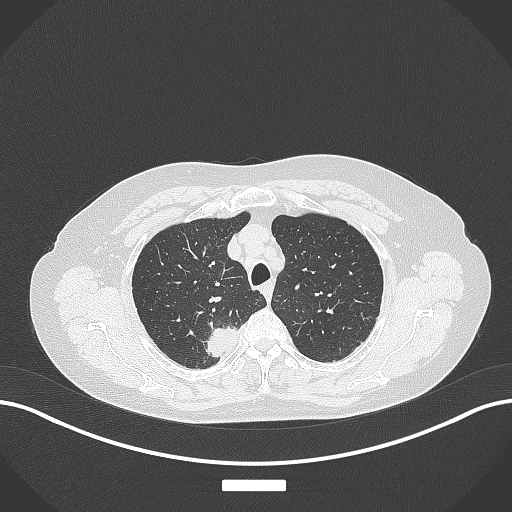
Chest CT, one axial slice. Position 314 of 357 along the scan axis. Reconstruction kernel B70f. 120 kVp. Lung window (W 1500 / L -600 HU). 1 mm slice thickness. 512 × 512 image matrix, field of view 400 × 400 mm. Patient: female, 62 years. From the clinical record (not read from this slice): clinical TNM (as recorded): T1c N1 M0.
Structures marked on this image (bounding box drawn by a radiologist):
- lung tumour (recorded histology: squamous cell carcinoma): bounding box (x1, y1, x2, y2) in pixels: (202, 325, 243, 367)